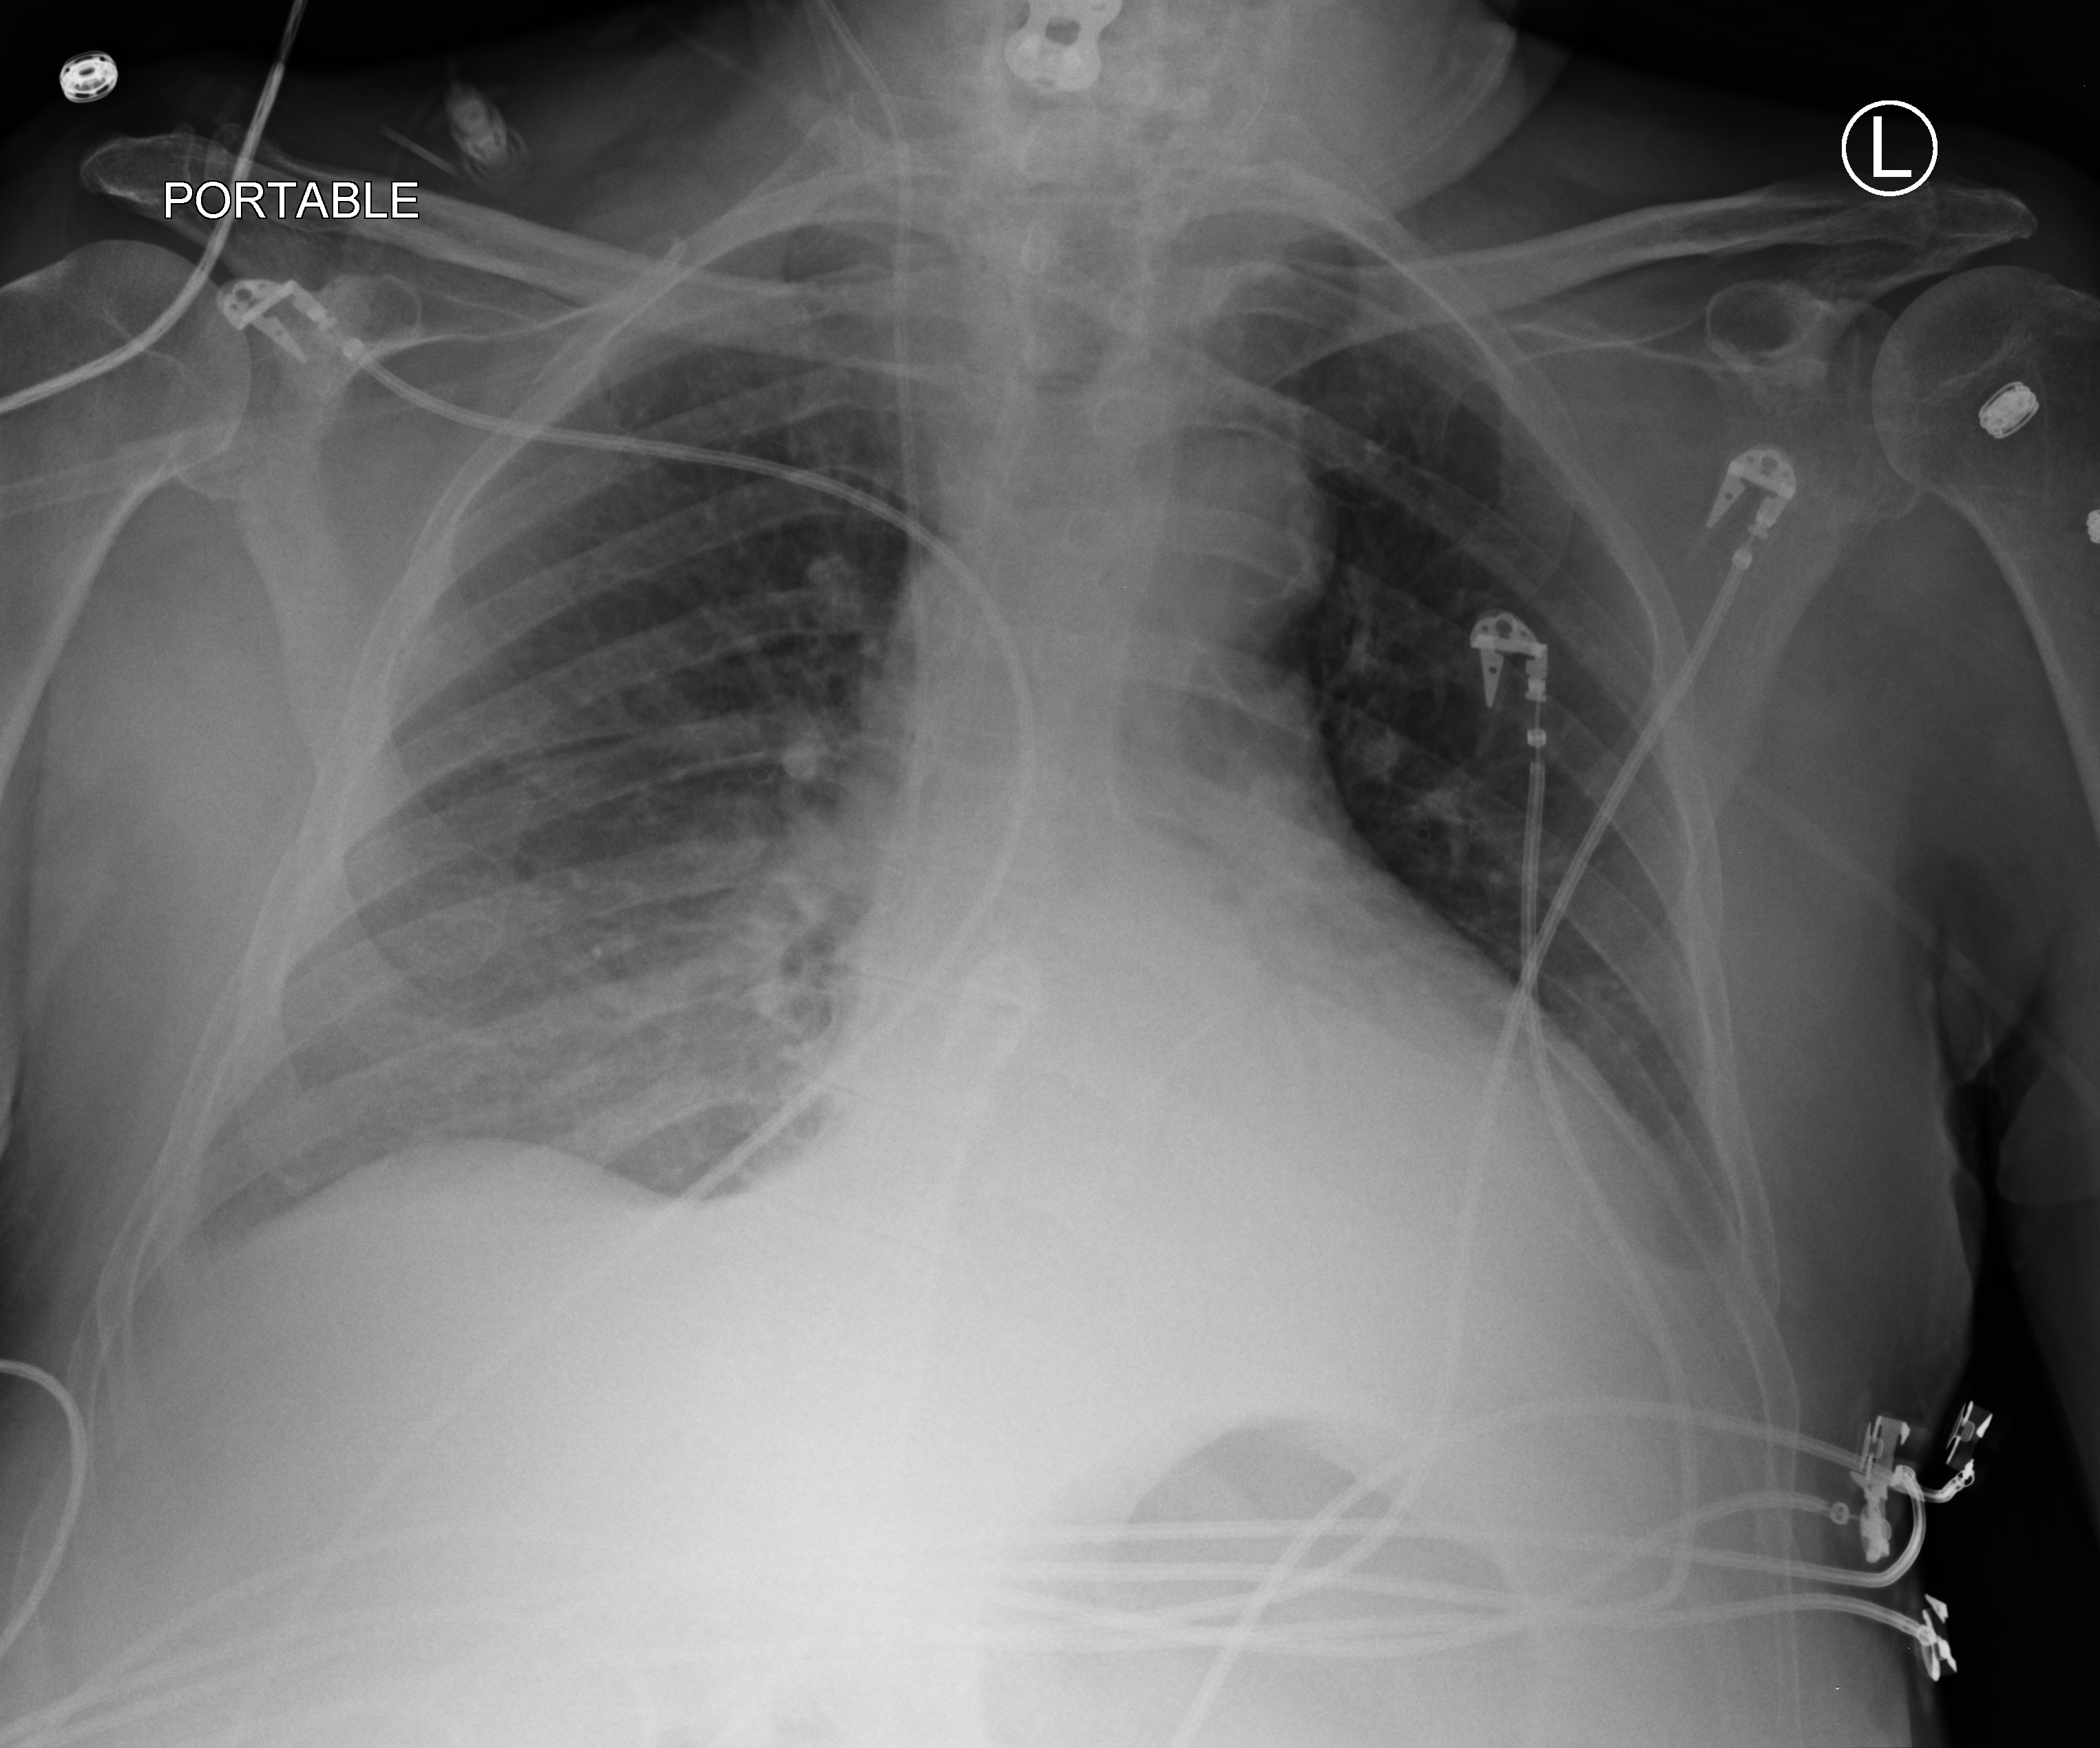
Chest X-ray (portable); anteroposterior (AP) projection. Patient hospitalised with COVID-19; male, aged 75–90 years.
Hospital-stay facts (about this admission, not read from this image; timing relative to this image not recorded):
- admitted to intensive care during this hospital stay: yes
- chronic kidney disease (admission record): no
- COPD (admission record): no